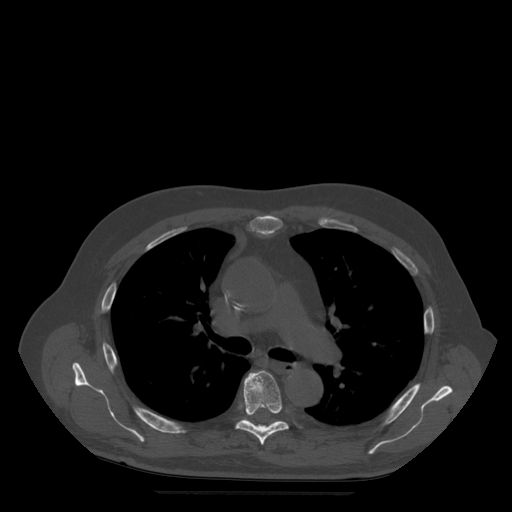
CT including the spine, one axial slice; bone window (W 1800 / L 400 HU); 1.25 mm slice thickness; 512 × 512 image matrix. Patient age 72 years. From the clinical record (not read from this slice): primary cancer: prostate.
Outlined on this slice (semi-automatically segmented with operator editing):
- T6 vertebra: box from (x=236, y=371) to (x=289, y=446) px
- T7 vertebra: (x=245, y=419)–(x=280, y=426)